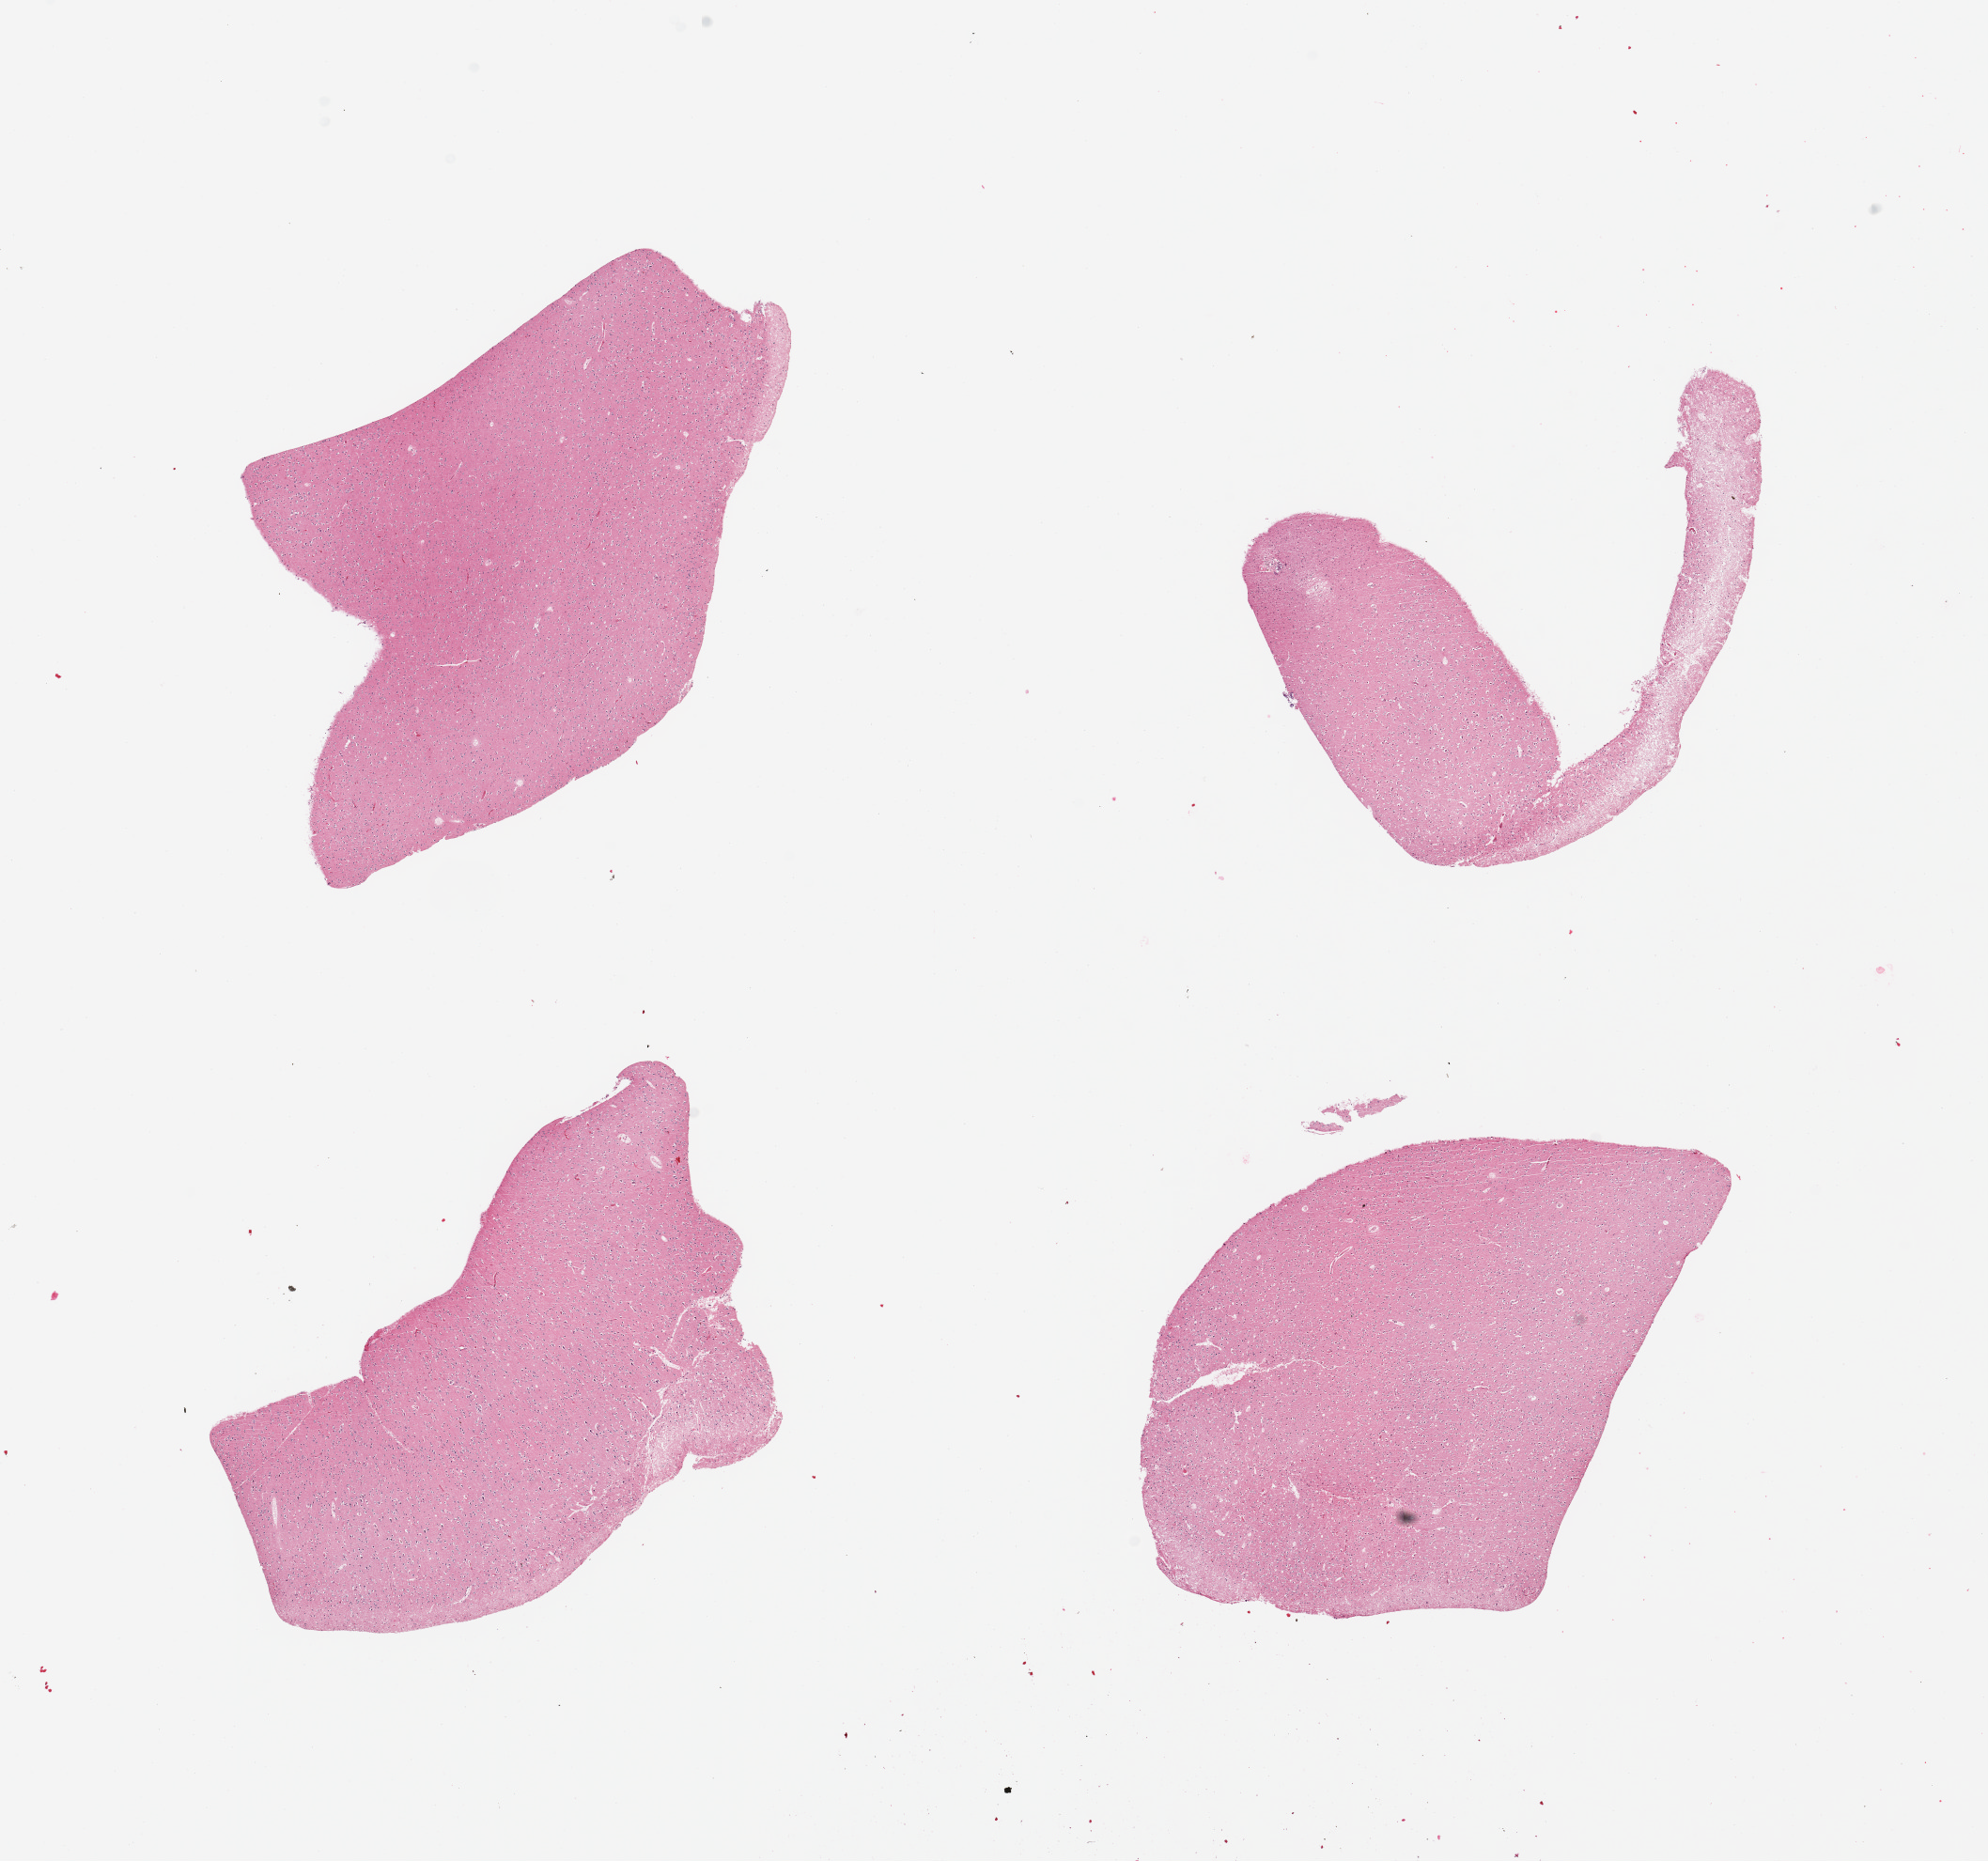
Digitized H&E-stained section — low-resolution overview of the scanned area, about 16.7 x 15.7 mm. PAXgene-fixed, paraffin-embedded tissue. Section of cerebral cortex (target tissue). Donor tissue sample. Donor: male.
Review note (as recorded): 4 pieces, no abnormalities.